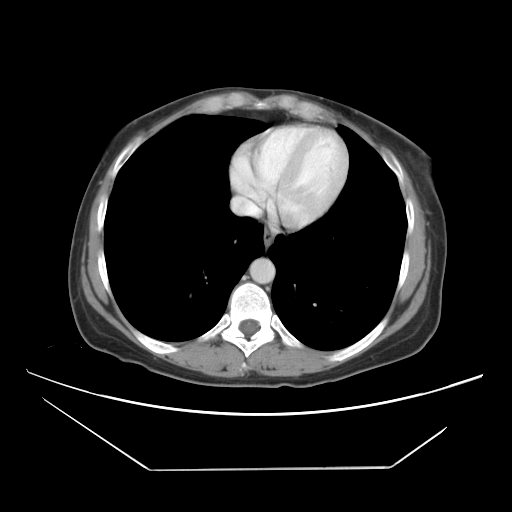
Contrast-enhanced abdominal CT, one axial slice. Position 41 of 42 along the scan axis. 120 kVp. Intravenous contrast given. Soft-tissue window (W 400 / L 40 HU). 5 mm slice thickness. 512 × 512 image matrix. Female patient, age 52 years. From the clinical record (not read from this slice): diagnosis: colorectal cancer liver metastases, imaged before liver resection; multiple liver metastases: yes; largest metastasis: 5.5 cm.
Structures marked on this image (outlined manually by an expert reader):
- hepatic veins: box from (x=233, y=129) to (x=288, y=215) px